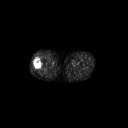
FDG PET of an extremity soft-tissue mass (from a PET/CT study), one axial slice; slice 235 of 267 in the series (ordered by position); 3.27 mm slice thickness; 128 × 128 image matrix, field of view 700 × 700 mm. Male patient, age 43 years. From the clinical record (not read from this slice): histological type: poorly differentiated synovial sarcoma; grade: high; site of the primary tumour: right buttock.
Outlined on this slice (expert contour drawn on MRI and transferred to this co-registered scan by the dataset authors):
- gross tumour volume including surrounding oedema: bounding box (x1, y1, x2, y2) in pixels: (33, 57, 42, 70)
- gross tumour volume (mass): (33, 59, 42, 70)